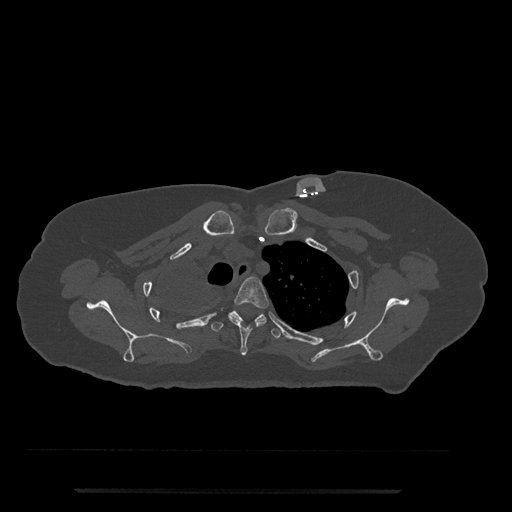
CT including the spine, one axial slice; slice 618 of 797 in the series (ordered by position); reconstruction kernel Br40s/3; 120 kVp; bone window (W 1800 / L 400 HU); 0.5 mm slice thickness; 512 × 512 image matrix, field of view 440 × 440 mm. Patient: female, 51 years. From the clinical record (not read from this slice): primary cancer: neuro; vertebrae with lytic lesions (as recorded): T8.
Annotated regions visible in this slice (semi-automatic segmentation, software-assisted and operator-edited):
- T3 vertebra: bounding box (x1, y1, x2, y2) in pixels: (228, 277, 269, 355)
- T4 vertebra: (211, 310, 282, 339)